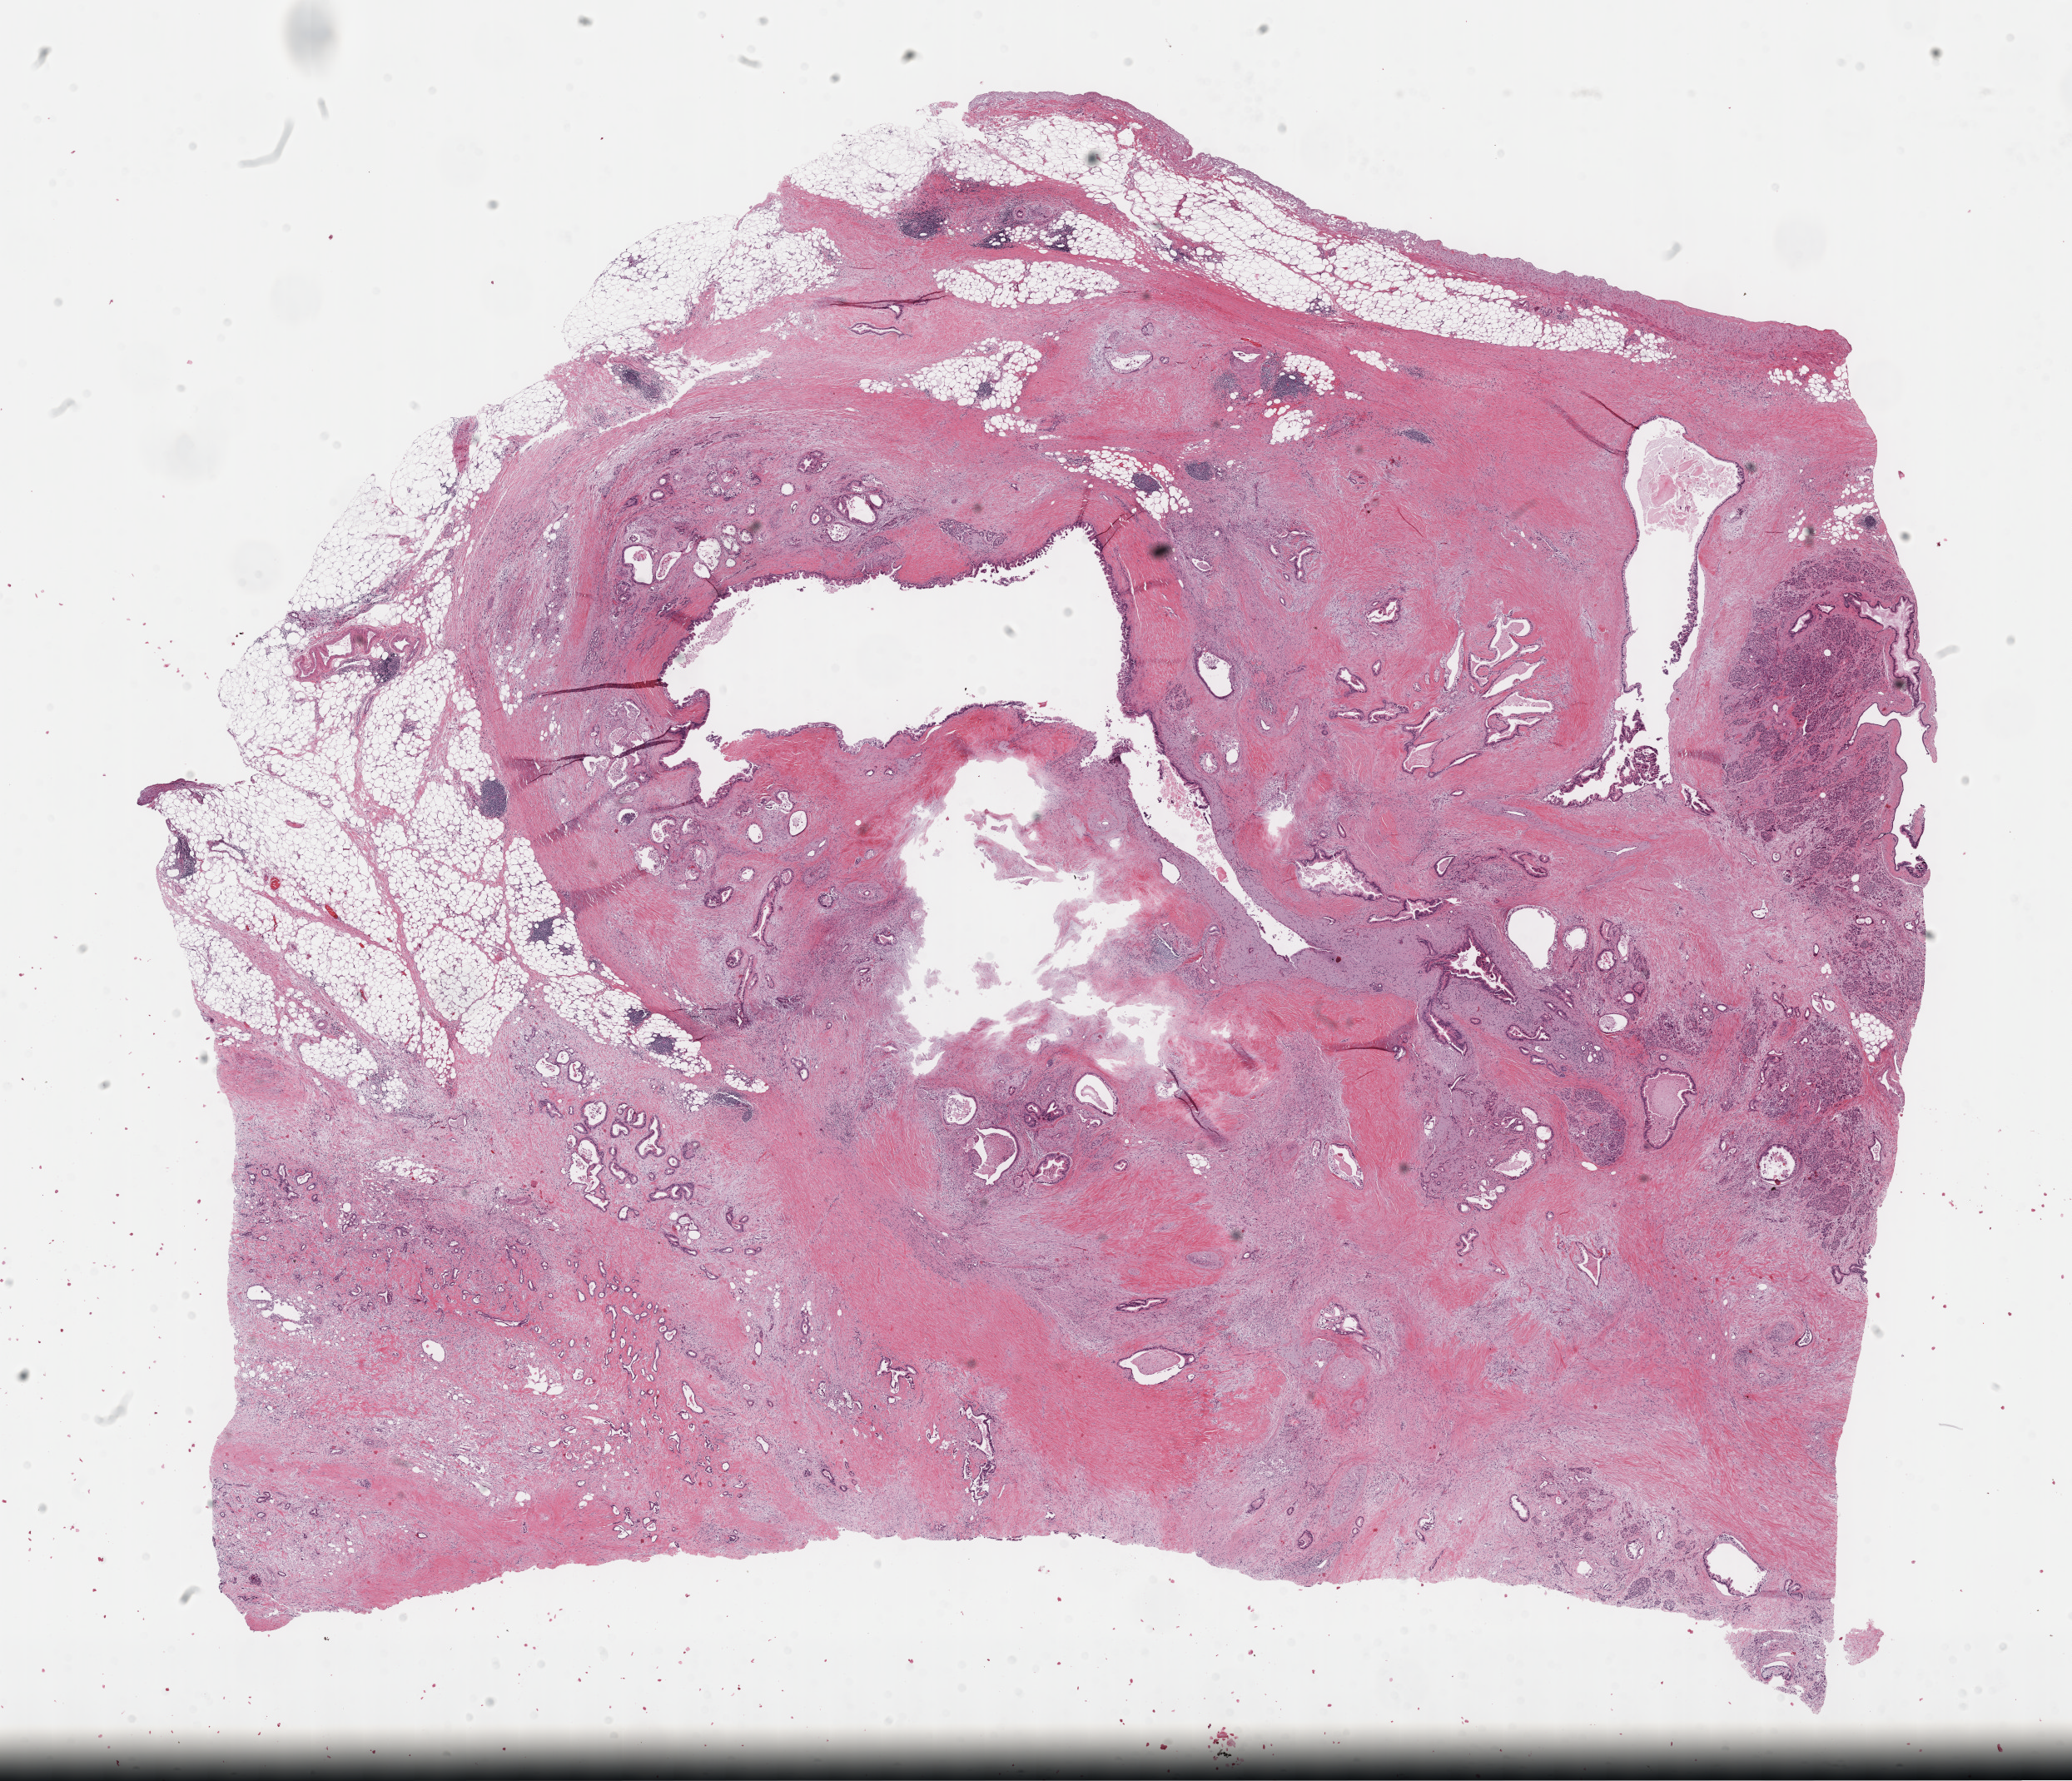
H&E whole-slide image, low-resolution overview of the scanned area, about 20.1 x 17.3 mm (acquisition: 40x scan). Formalin-fixed paraffin-embedded (FFPE) diagnostic section. Primary tumour sample from the pancreas. Male, age 71 years at initial diagnosis. Histologic grade: G2 (moderately differentiated).
- AJCC pathologic stage: IIB
- lymph nodes positive (case pathology): 2 of 19 examined
- histologic diagnosis: Infiltrating duct carcinoma, NOS (head of pancreas)